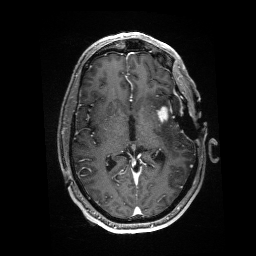
Brain MRI from a brain-tumour surgery series, one axial slice. Position 87 of 176 along the scan axis. T1-weighted post-contrast. 1 mm slice thickness. 256 × 256 image matrix. Case-level facts recorded for this patient, not image findings: histopathology: Glioblastoma; WHO grade: 4; IDH mutation: no.
Structures marked on this image (outlined manually by an expert reader):
- residual tumour: box from (x=157, y=106) to (x=169, y=122) px